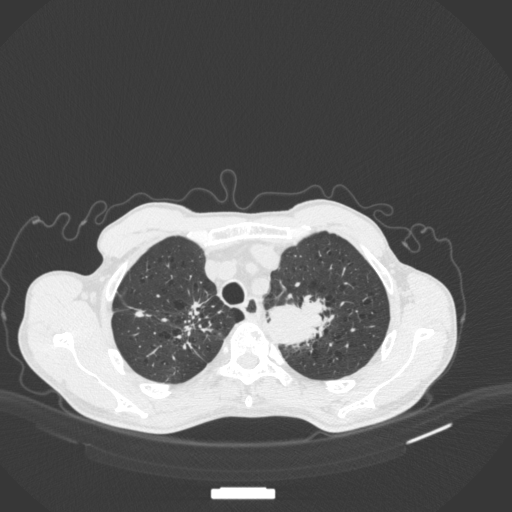
Chest CT, one axial slice; slice 352 of 394 in the series (ordered by position); reconstruction kernel B31f; lung window (W 1500 / L -600 HU); 1 mm slice thickness; 512 × 512 image matrix, field of view 400 × 400 mm. Patient: male, 65 years. Case-level facts recorded for this patient, not image findings: clinical TNM (as recorded): T2b N0 M0.
Structures marked on this image (bounding box drawn by a radiologist):
- lung tumour (recorded histology: adenocarcinoma): bounding box <268,283,339,347> (left, top, right, bottom; pixels)